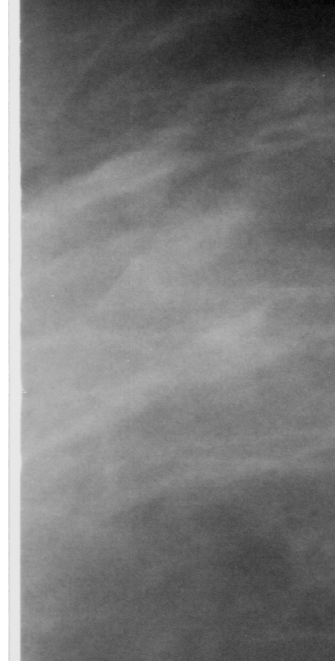
Crop from a digitized film mammogram around one marked abnormality, left breast, CC view.
- Finding: mass, shape asymmetric breast tissue; BI-RADS assessment category 3; benign; no additional work-up was recommended (benign without callback).